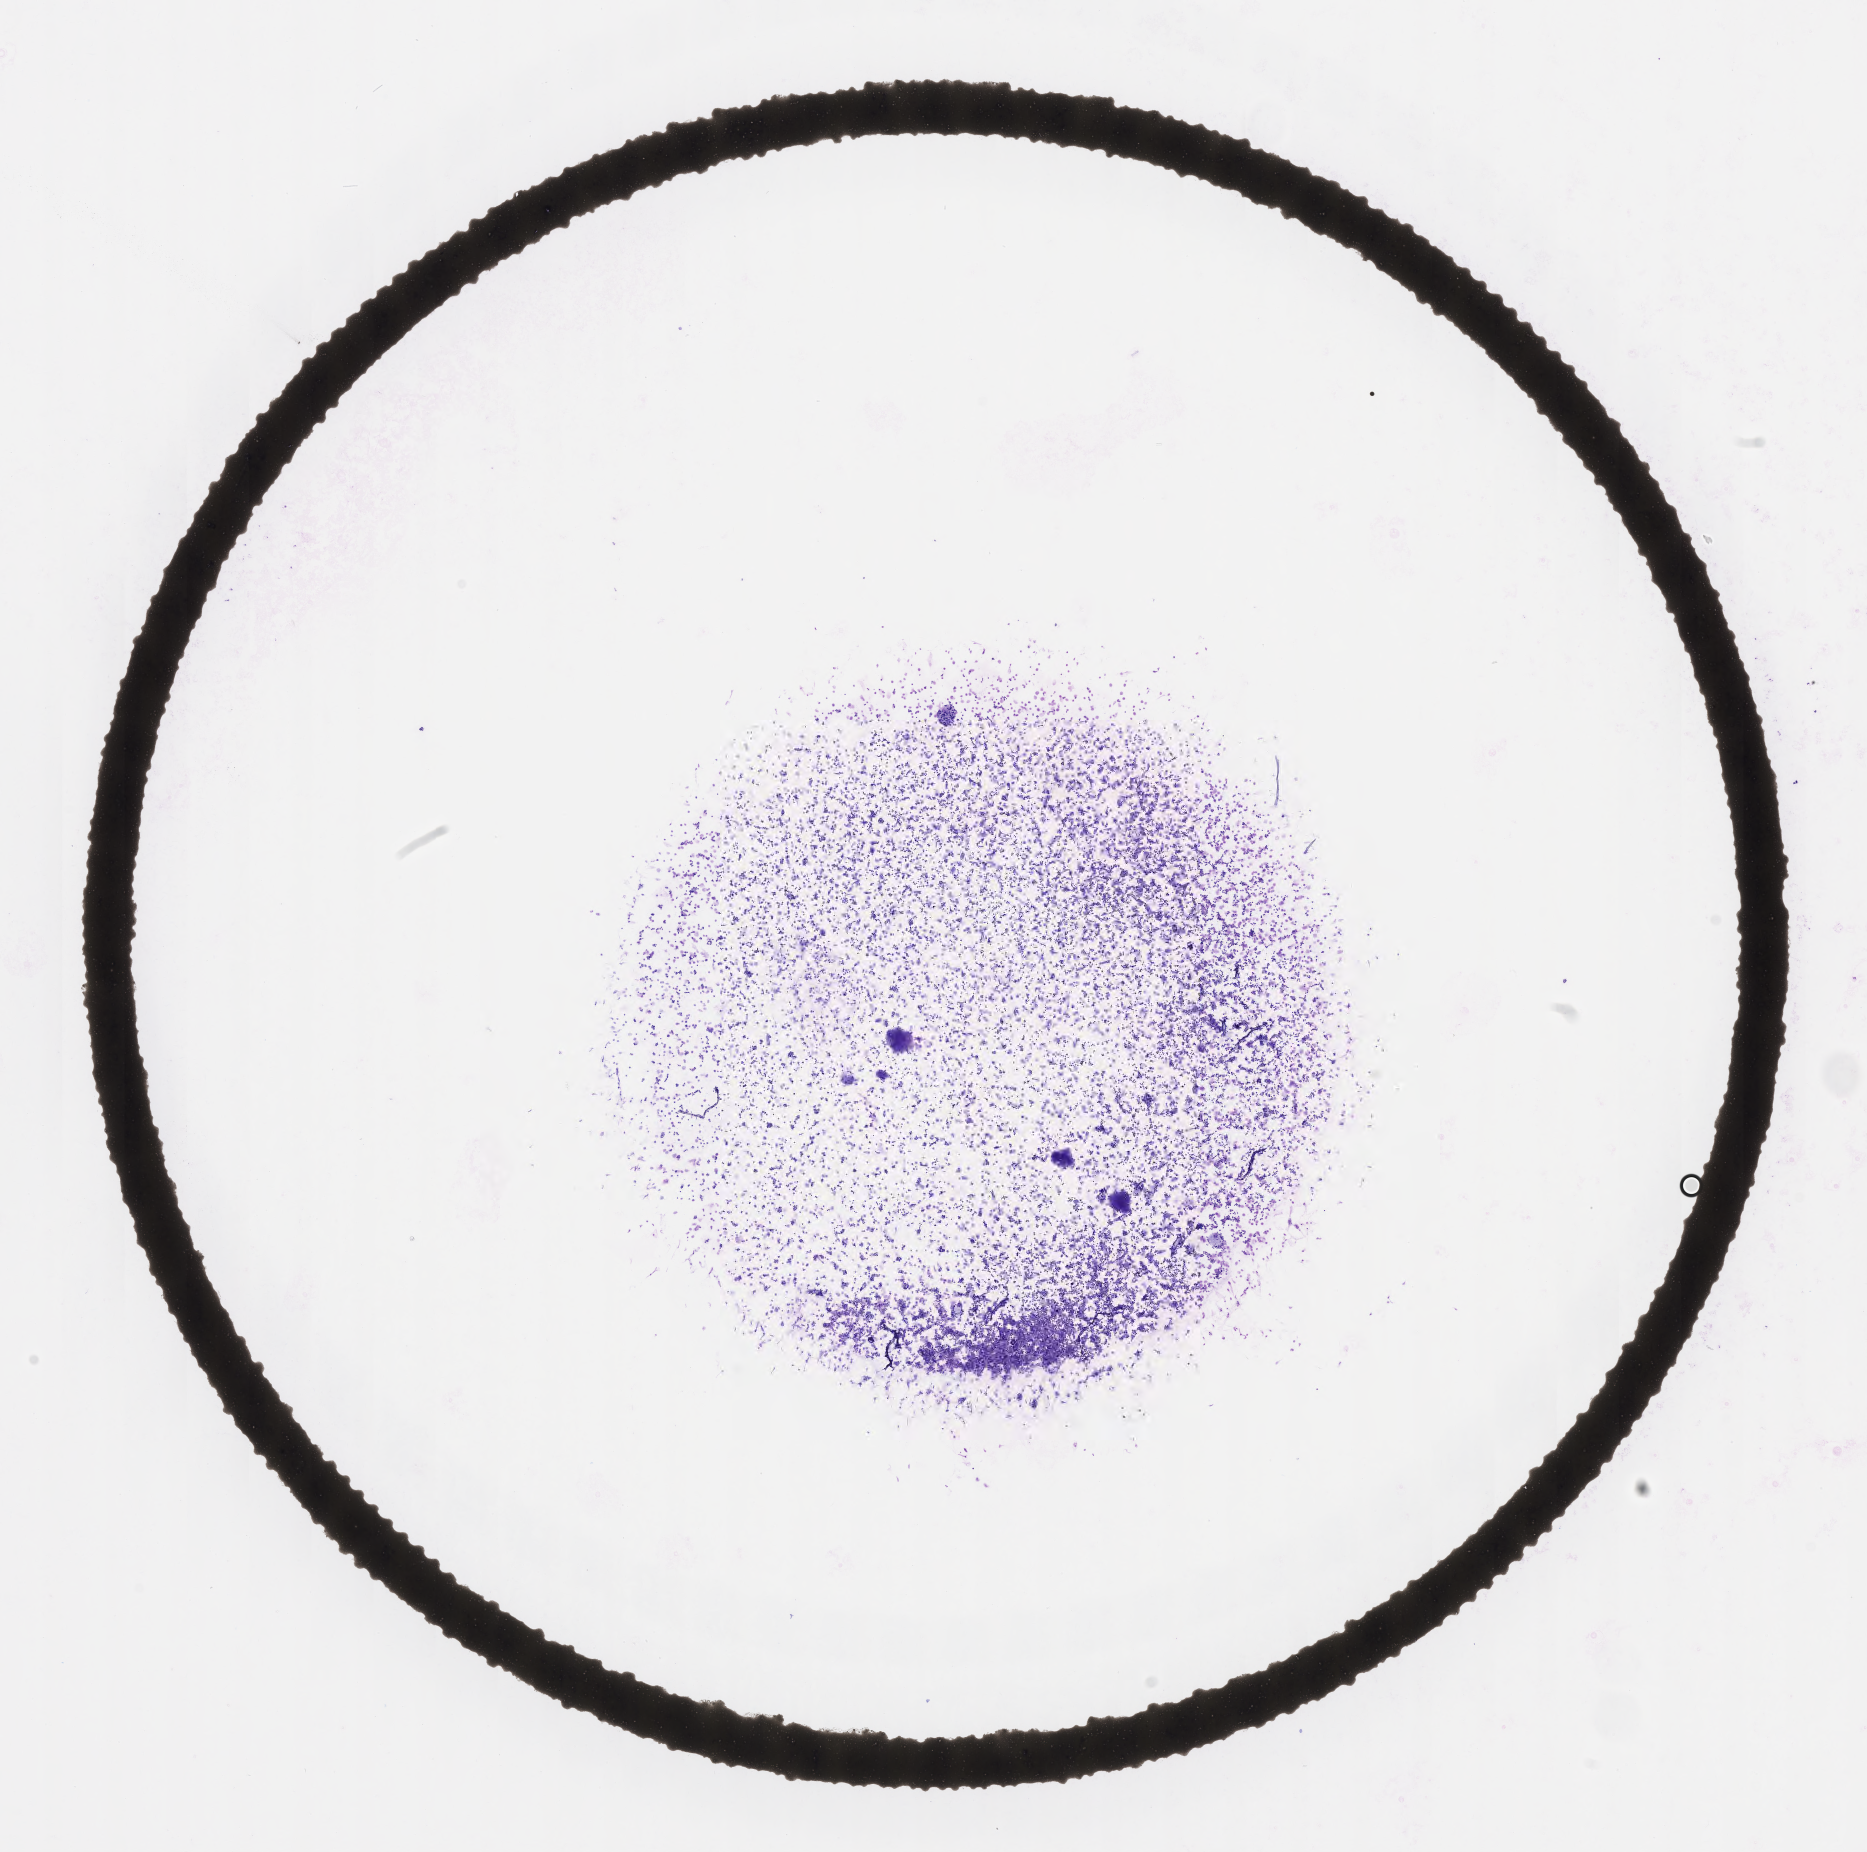
Whole-slide image of tumor tissue from the retroperitoneum — shown as a low-resolution overview of the whole scanned area (about 15.1 x 15.0 mm). Male patient, age 50 months (4 years 2 months).
Diagnosis (ICD-O-3 morphology term): Neuroblastoma, NOS.